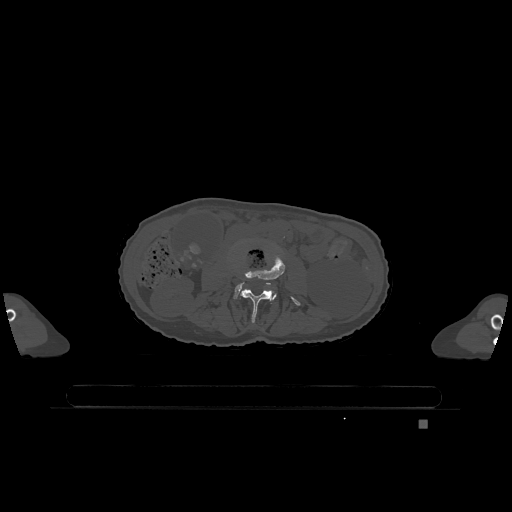
CT including the spine, one axial slice; slice 344 of 1317 in the series (ordered by position); bone window (W 1800 / L 400 HU); 0.5 mm slice thickness; 512 × 512 image matrix. Patient: female, 74 years. From the clinical record (not read from this slice): primary cancer: lung.
Structures marked on this image (semi-automatic segmentation, software-assisted and operator-edited):
- L3 vertebra: bounding box [x1, y1, x2, y2] px = [240, 255, 301, 322]
- L4 vertebra: [234, 282, 277, 300]